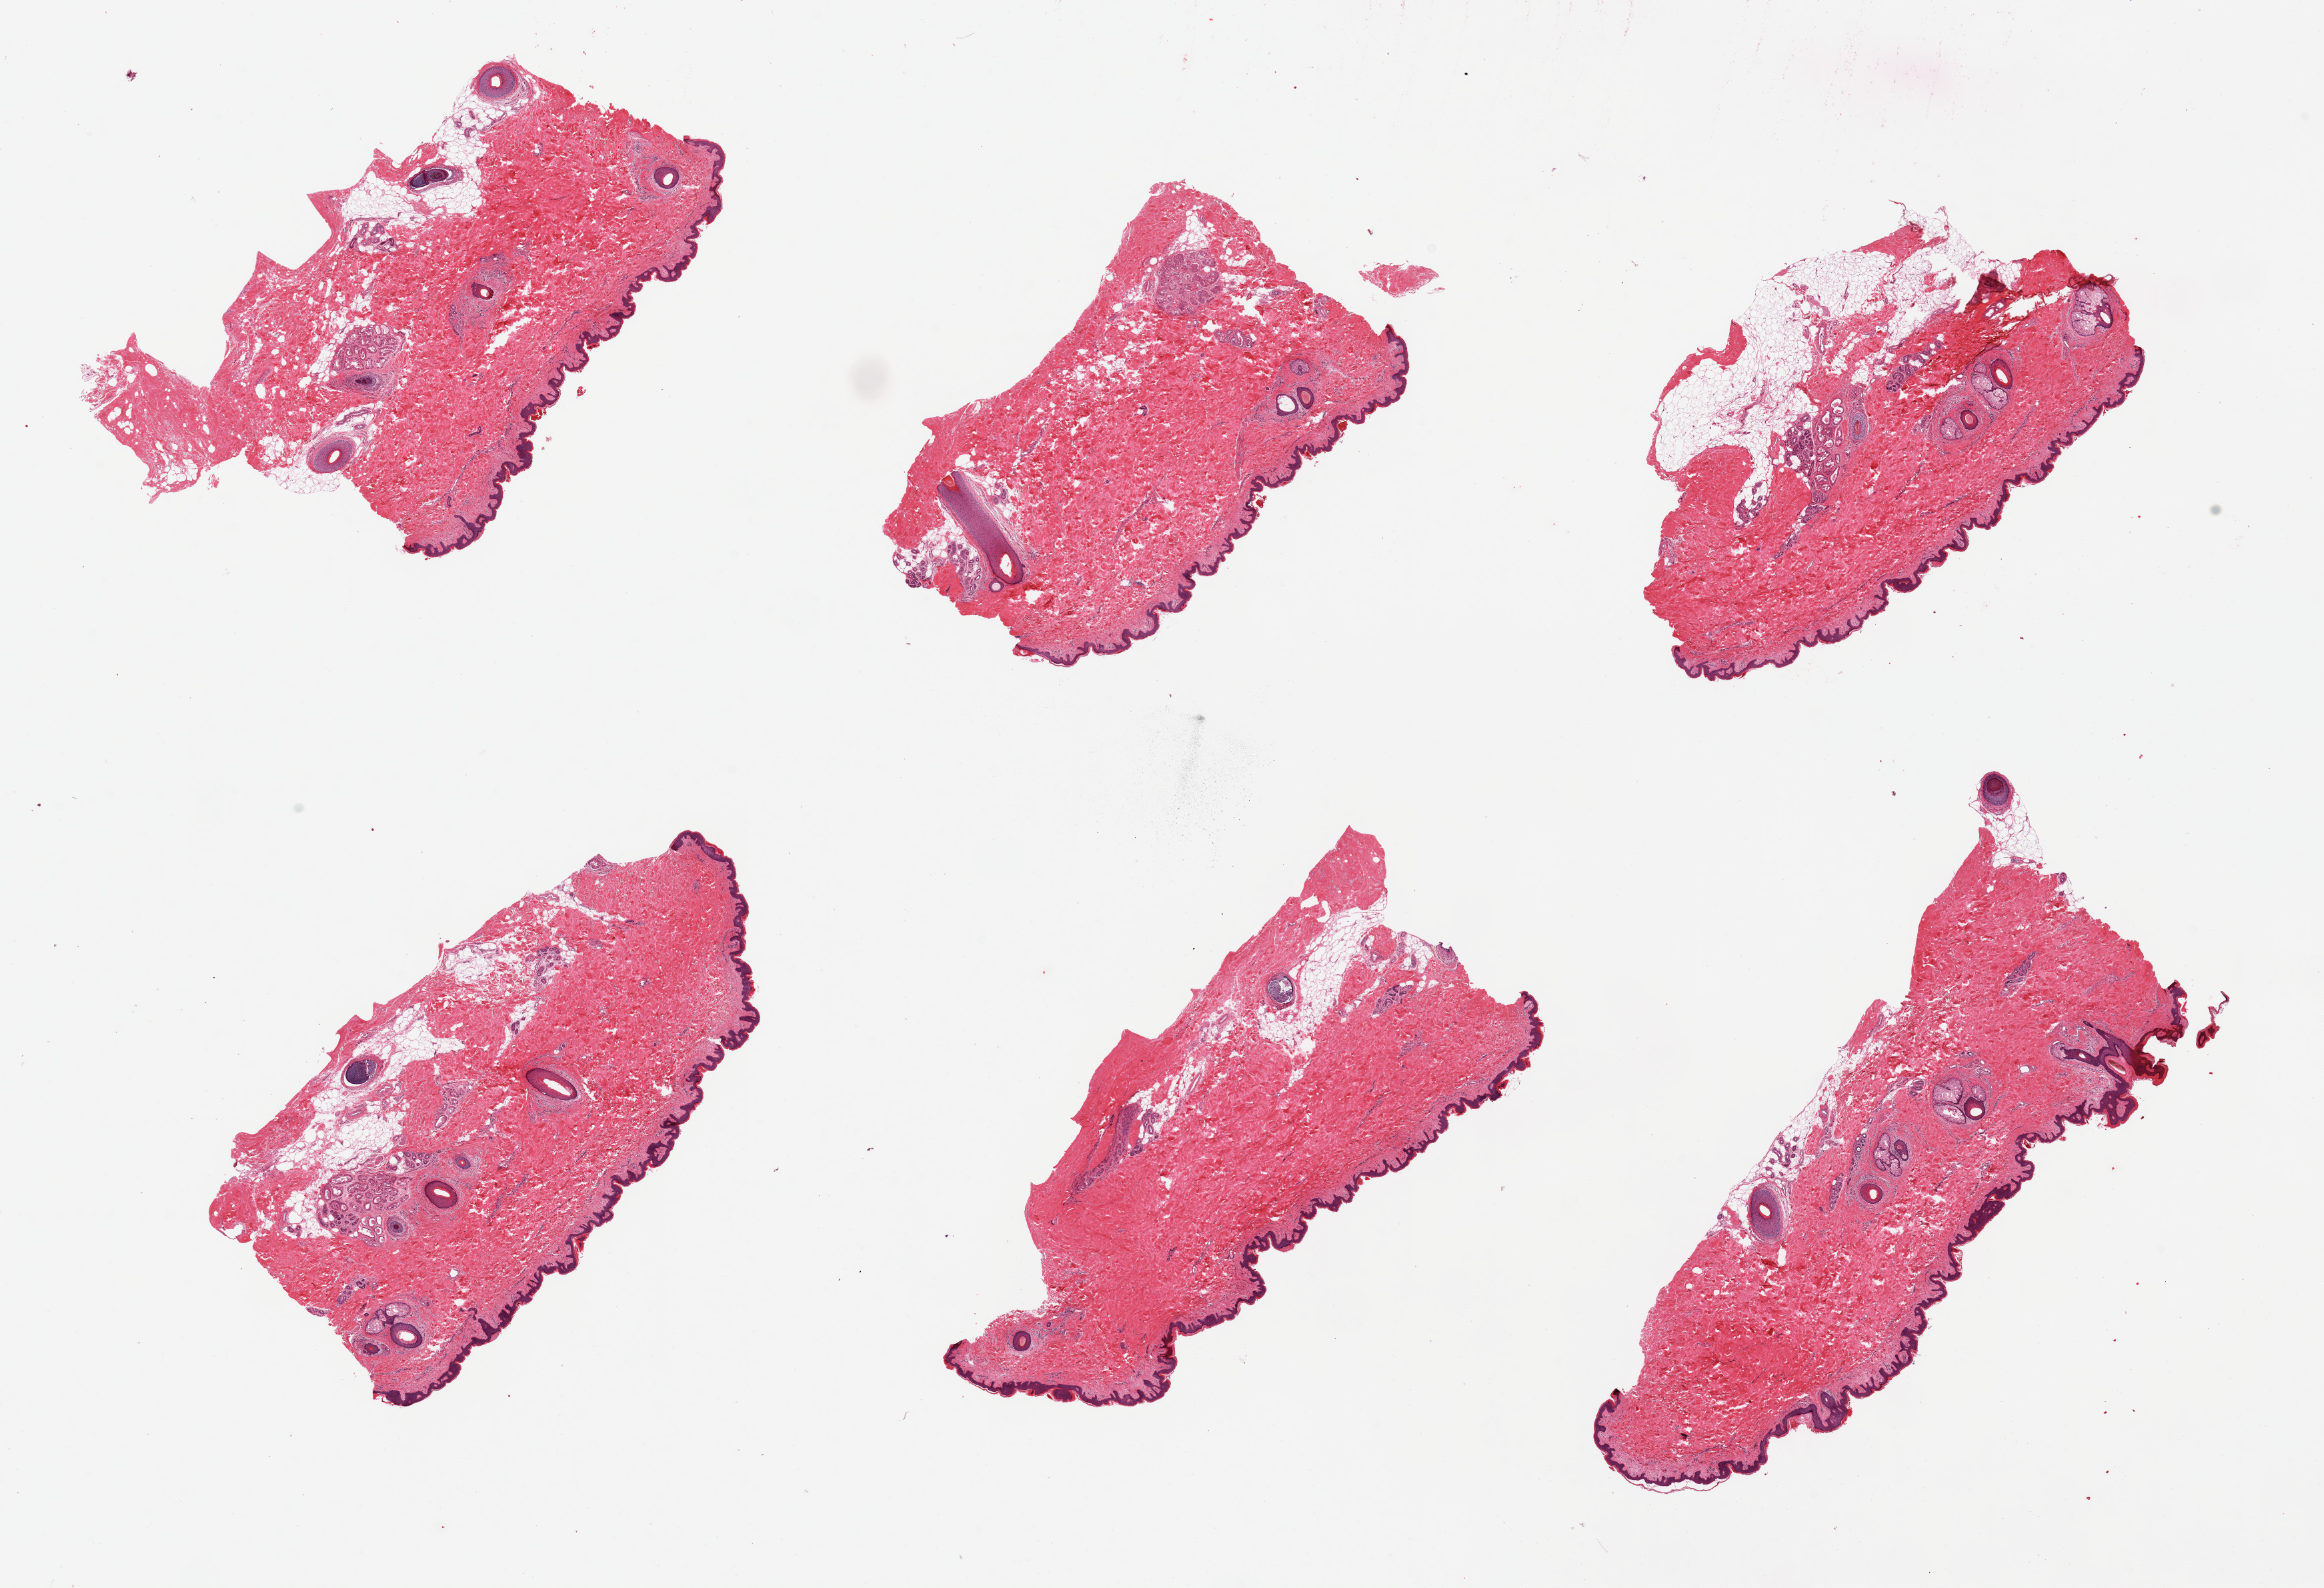
Hematoxylin and eosin (H&E) whole-slide image — whole scanned area (about 27.6 x 18.8 mm, acquisition: 20x scan) shown as a low-resolution overview; PAXgene-fixed paraffin-embedded (PFPE) section; target tissue: skin of suprapubic region; donor tissue sample. Male donor.
- review note (as recorded): 6 pieces of hair-bearing skin; well trimmed except for one with 1 mm fat